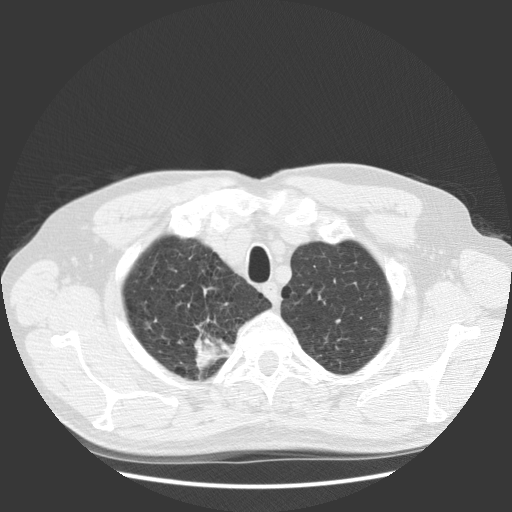
Chest CT (low-dose screening protocol), one axial image, baseline screening round, lung window (W 1500 / L -600 HU), 2.5 mm slice thickness, standard (soft-tissue) reconstruction kernel (STANDARD), 512 × 512 image matrix, field of view 369 × 369 mm. Male participant, aged 63 years at enrolment. Current smoker at enrolment.
Expert-annotated lung lesion, box from (x=170, y=324) to (x=241, y=385) px. The screening reader recorded 2 non-calcified nodules or masses ≥4 mm on this exam (right upper lobe, right upper lobe); which of them this box marks is not recorded.